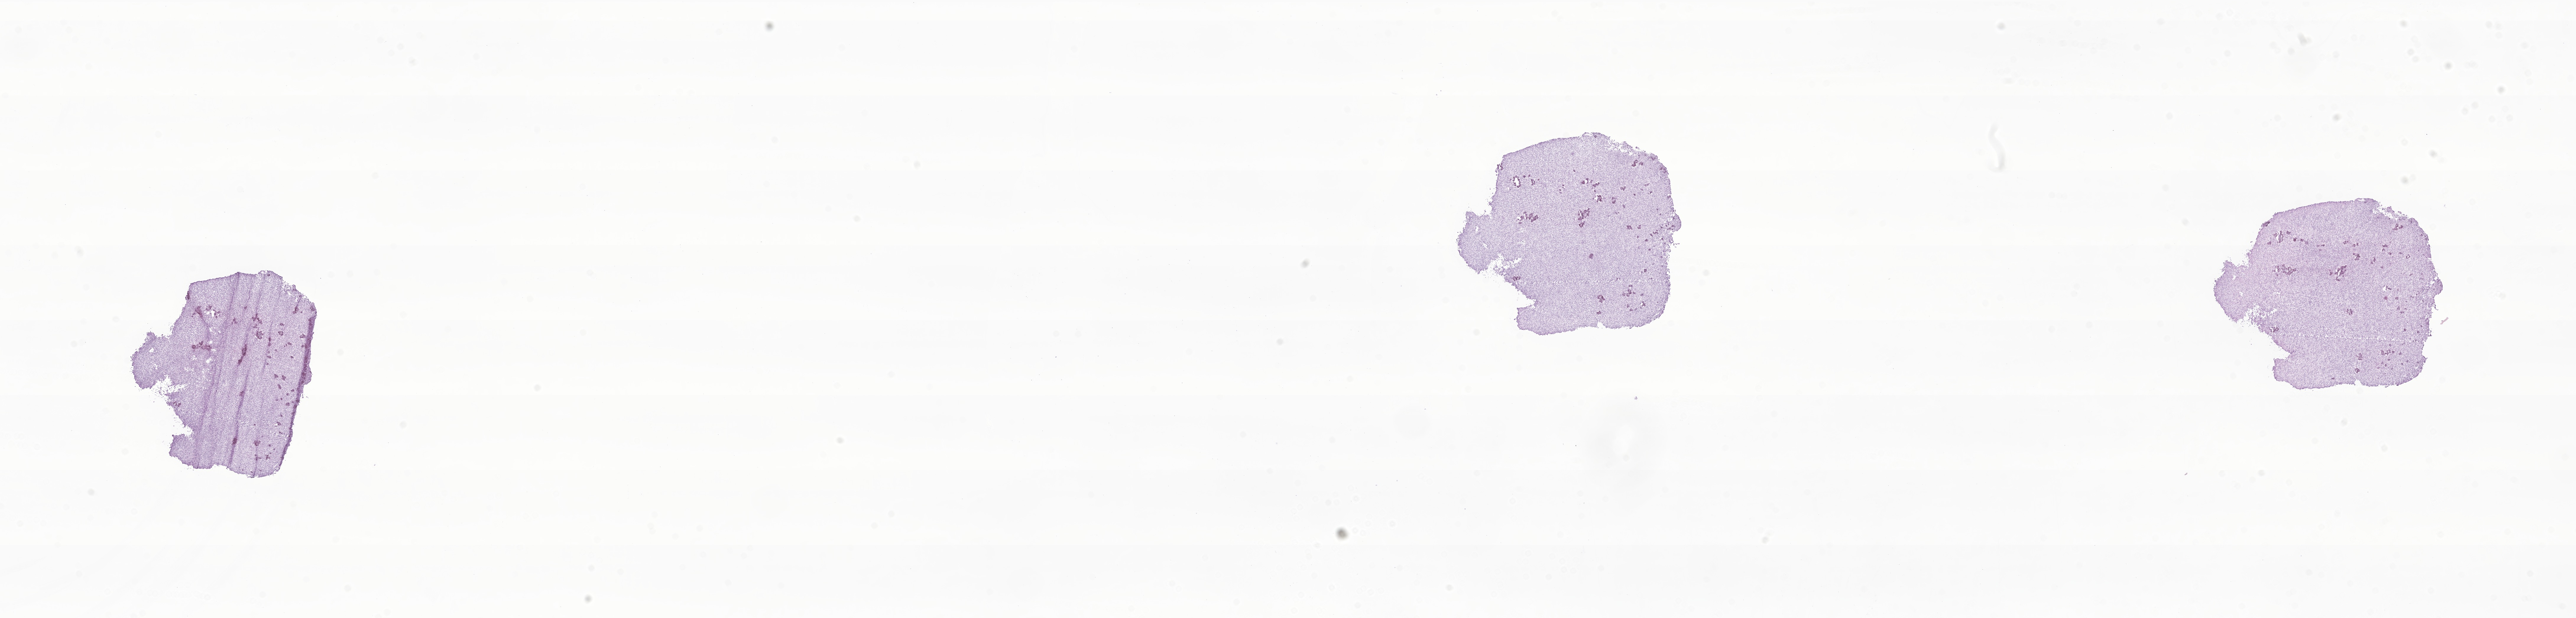
Hematoxylin and eosin (H&E) whole-slide image of tumor tissue from the brain, whole scanned area (about 36.7 x 8.8 mm) shown as a low-resolution overview, frozen section. Female patient, age 253 months.
Recorded diagnosis: Glioma, malignant.